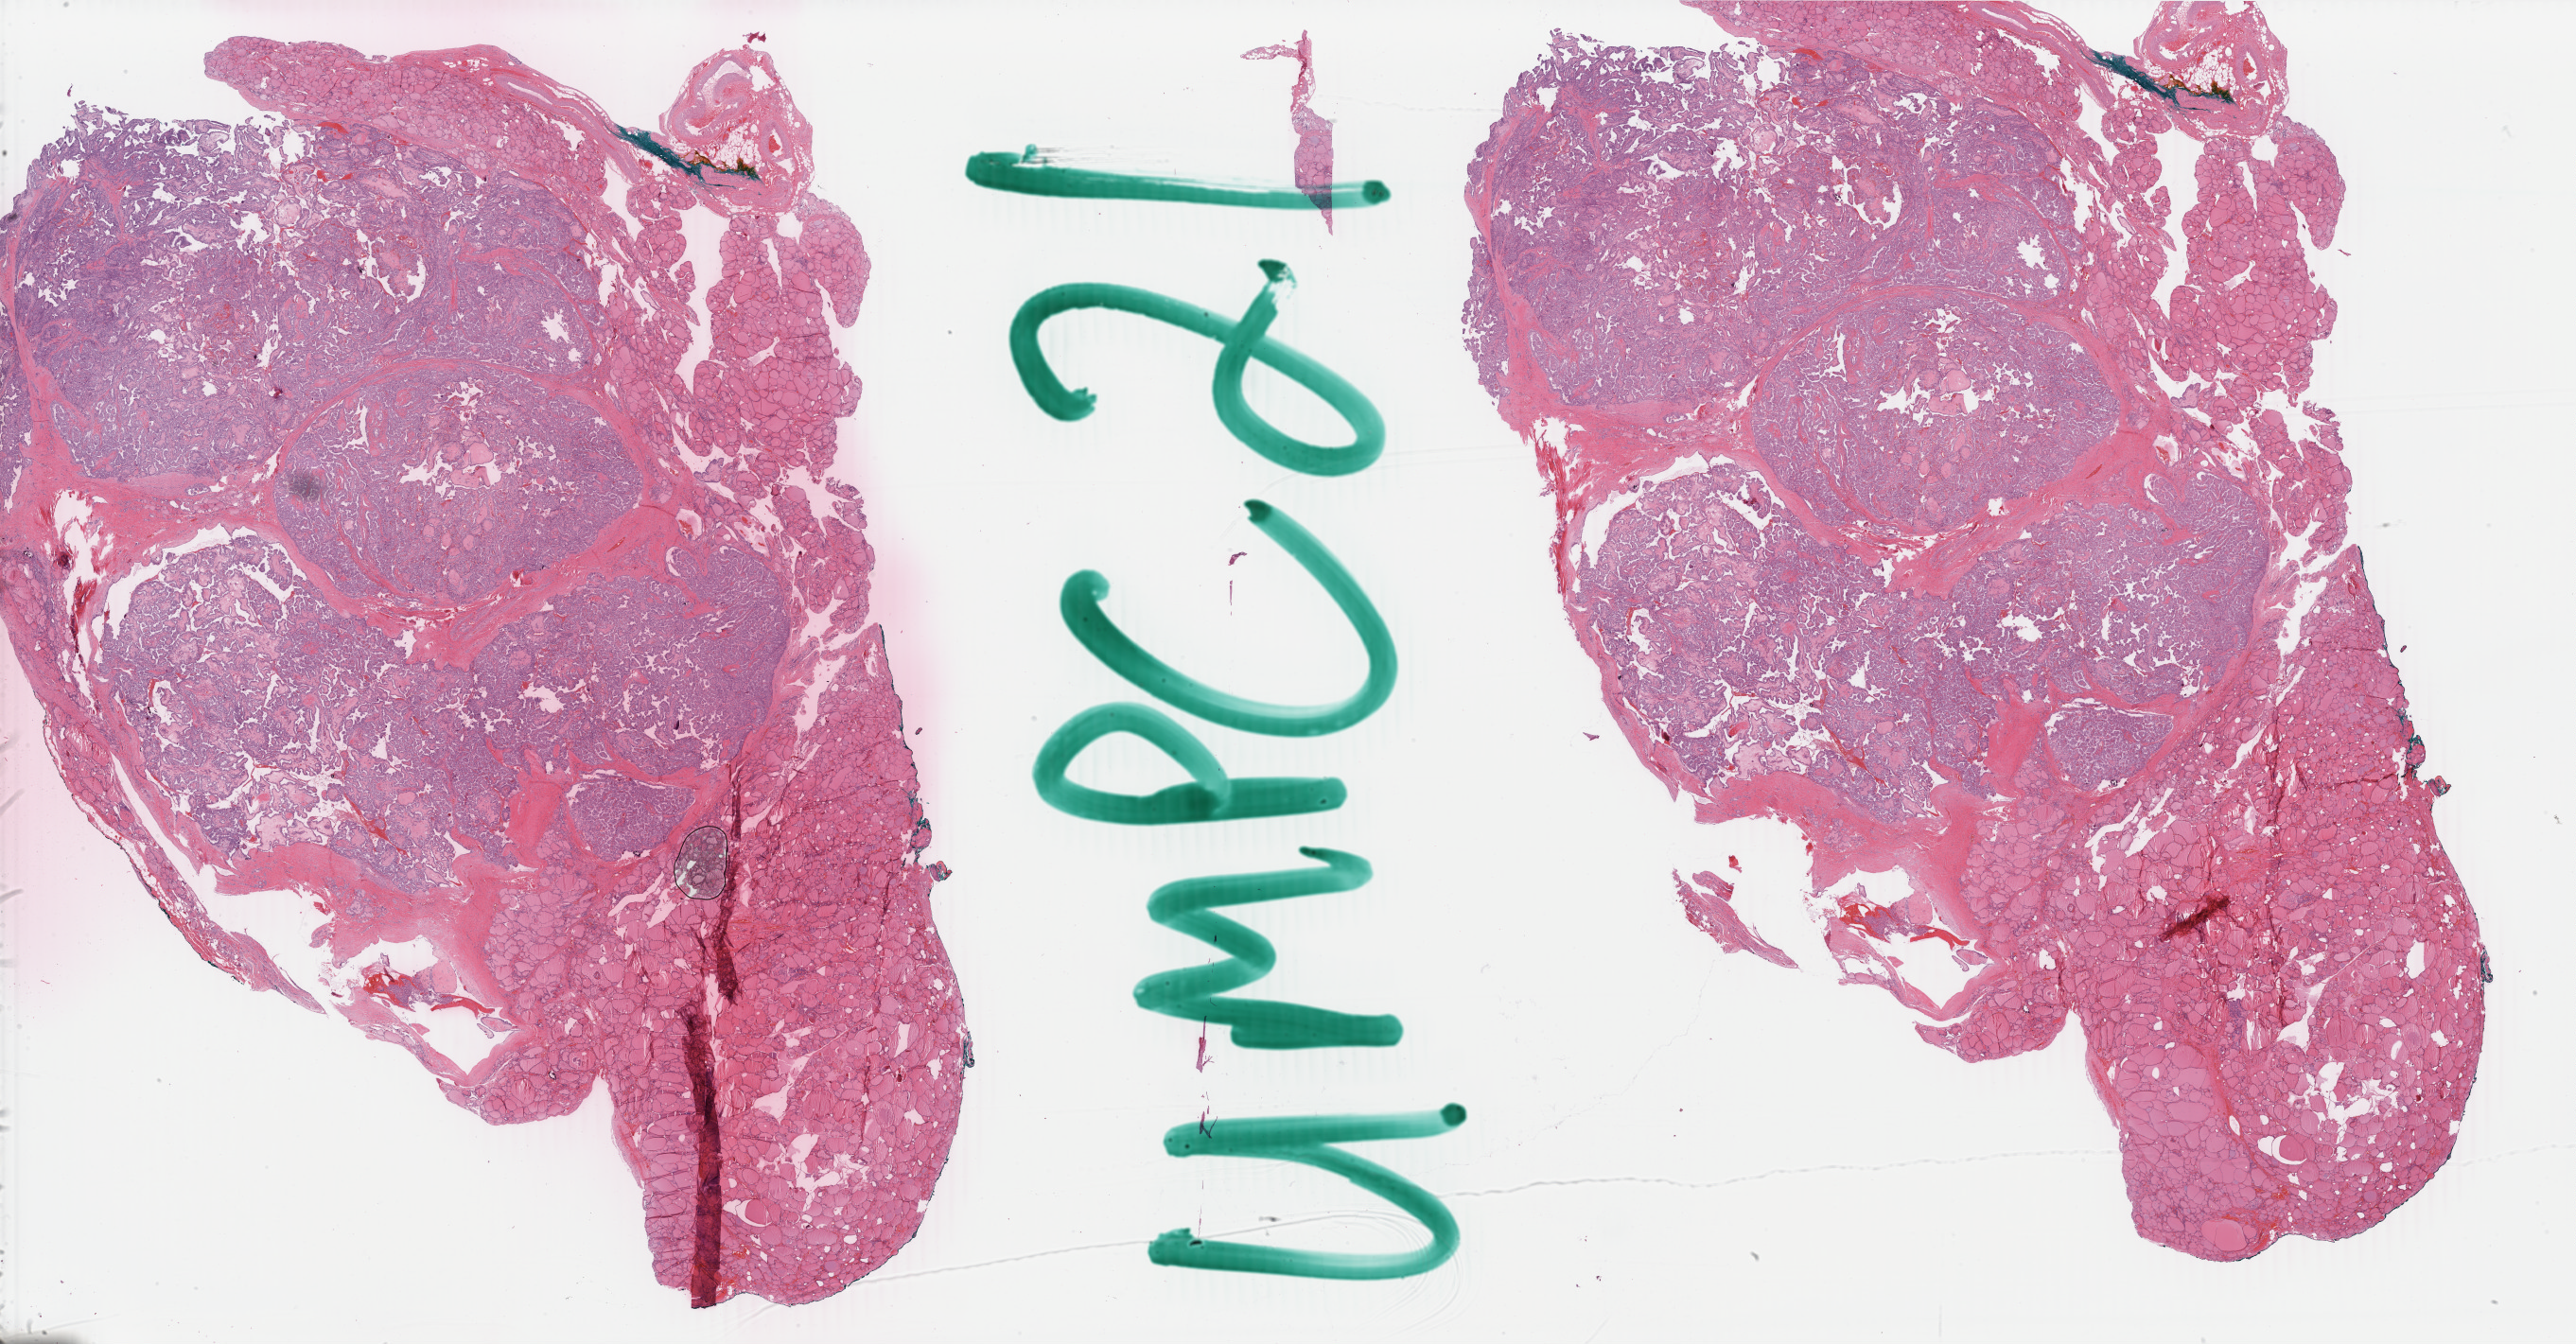
Digitized Hematoxylin and eosin (H&E) stained tissue section (whole slide), shown as a low-resolution overview of the whole scanned area (about 43.3 x 22.6 mm), formalin-fixed paraffin-embedded (FFPE) diagnostic section, thyroid, primary tumour sample. Female, age 49 years at initial diagnosis.
Lymph nodes positive (case pathology): 0 of 2 examined. Laterality: right. AJCC pathologic stage: IVA. Pathologic diagnosis: Papillary adenocarcinoma, NOS (thyroid gland).